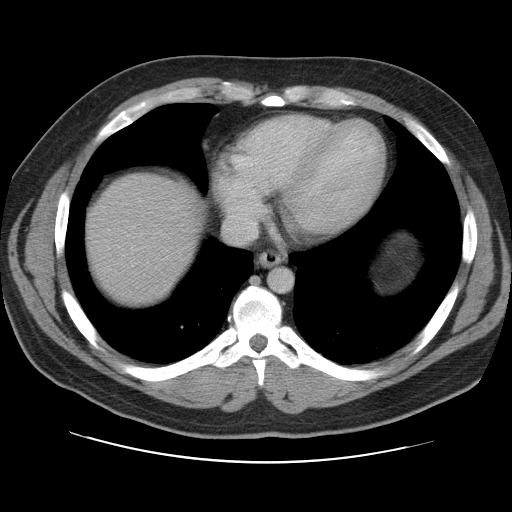
Contrast-enhanced abdominal CT, one axial slice; slice 101 of 109 in the series (ordered by position); intravenous contrast given; soft-tissue window (W 400 / L 40 HU); 5 mm slice thickness; 512 × 512 image matrix, field of view 402 × 402 mm. Male patient, age 35 years. Case-level facts recorded for this patient, not image findings: diagnosis: colorectal cancer liver metastases, imaged before liver resection; multiple liver metastases: yes; largest metastasis: 2.8 cm; disease in both lobes: yes.
Outlined on this slice (expert manual segmentation):
- liver: bounding box <85,174,202,309> (left, top, right, bottom; pixels)
- planned liver remnant (the part of the liver to remain after resection): <85,174,202,307>